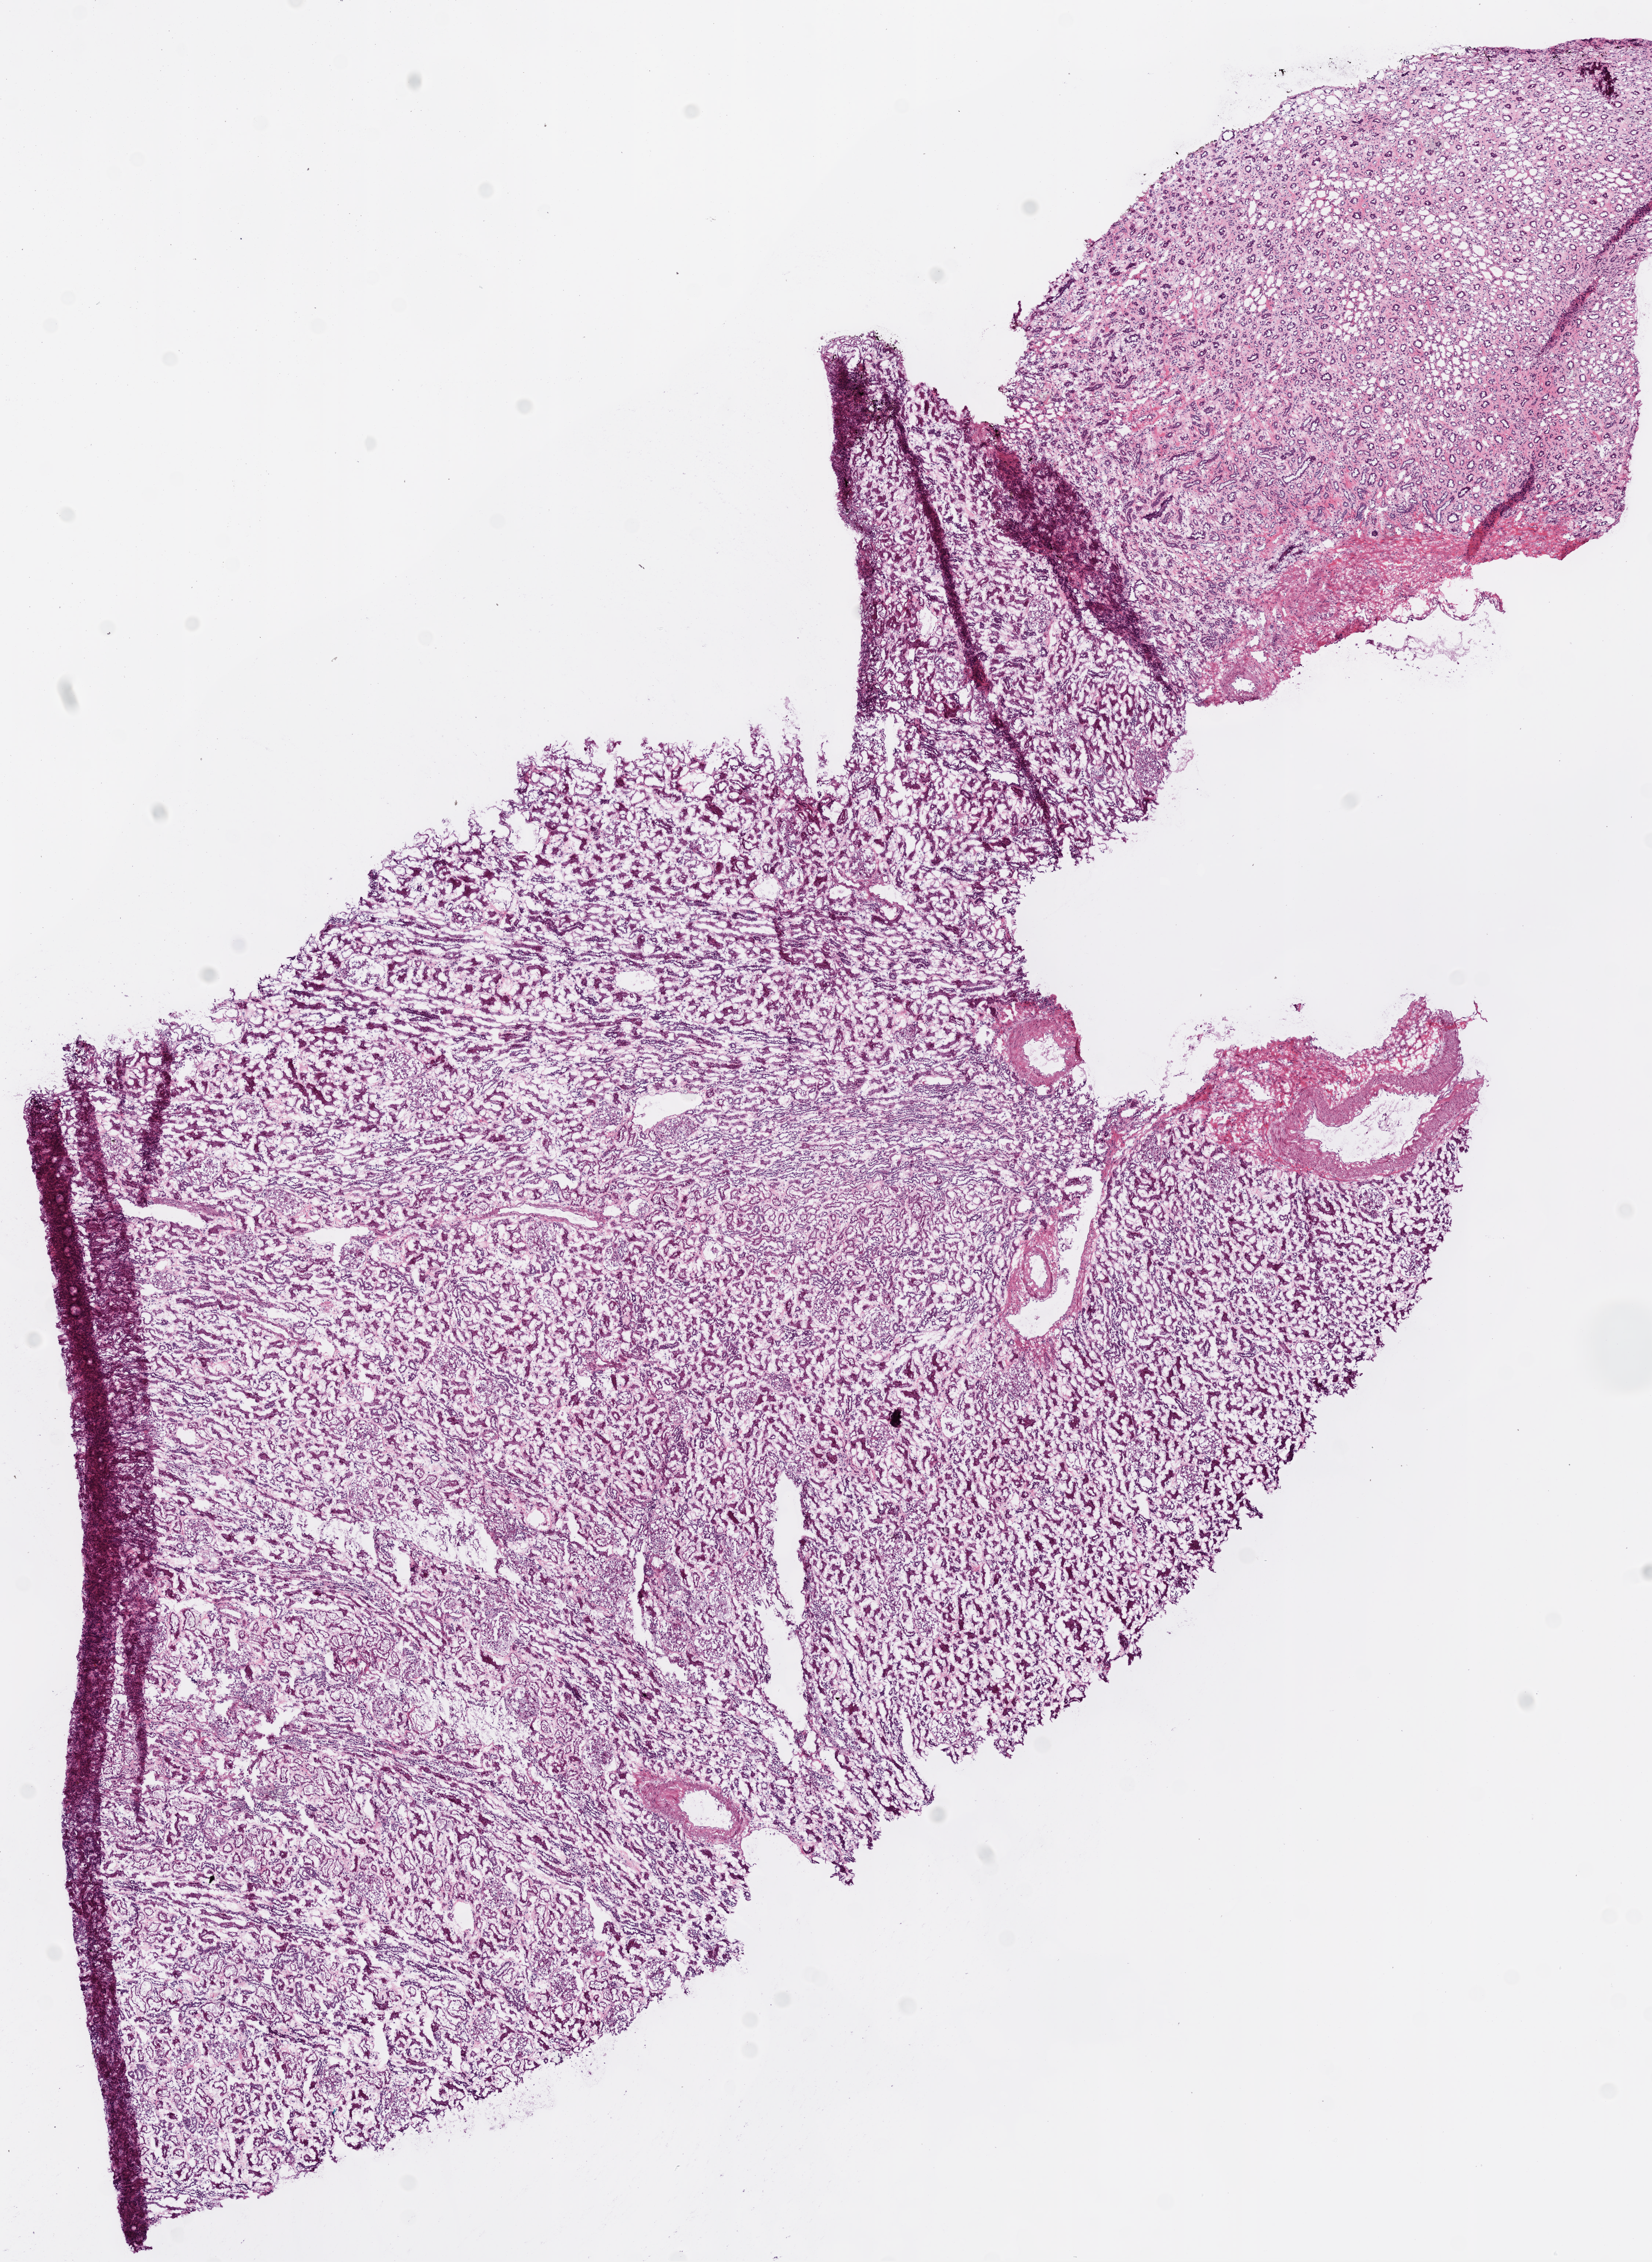
Whole-slide histology image, H&E-stained — whole scanned area (about 9.0 x 12.4 mm) shown as a low-resolution overview; frozen section from the top of the tissue portion; kidney, solid tissue normal (non-tumour tissue) sample. Patient: female, age at initial diagnosis 48 years.
This section: solid tissue normal (non-tumour) sample from the same patient. Patient diagnosis: Clear cell adenocarcinoma, NOS.